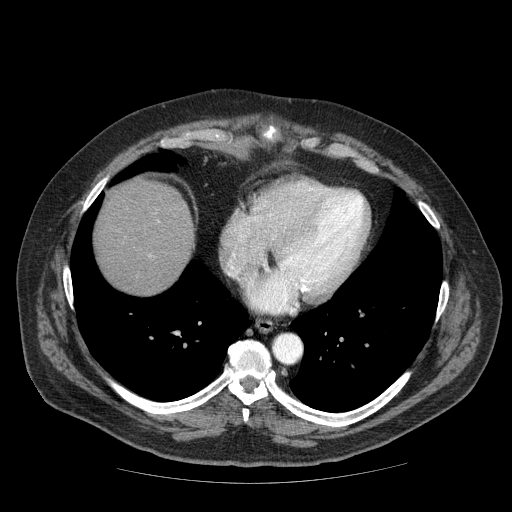
Contrast-enhanced abdominal CT (liver protocol), one axial slice. Slice 68 of 85 in the series (ordered by position). Reconstruction kernel STANDARD. 120 kVp. Soft-tissue window (W 400 / L 40 HU). 2.5 mm slice thickness. 512 × 512 image matrix, field of view 420 × 420 mm. From the clinical record (not read from this slice): diagnosis: hepatocellular carcinoma (patient treated with transarterial chemoembolisation; whether this scan precedes or follows treatment is not stated here); TNM stage (as recorded): Stage-IIIA; Child-Pugh class: A.
Structures marked on this image (semi-automatic segmentation, software-assisted and operator-edited):
- liver parenchyma outside the tumour (the mass and vessels are separate outlines, so this box may not span the whole liver): bounding box <94,178,194,294> (left, top, right, bottom; pixels)